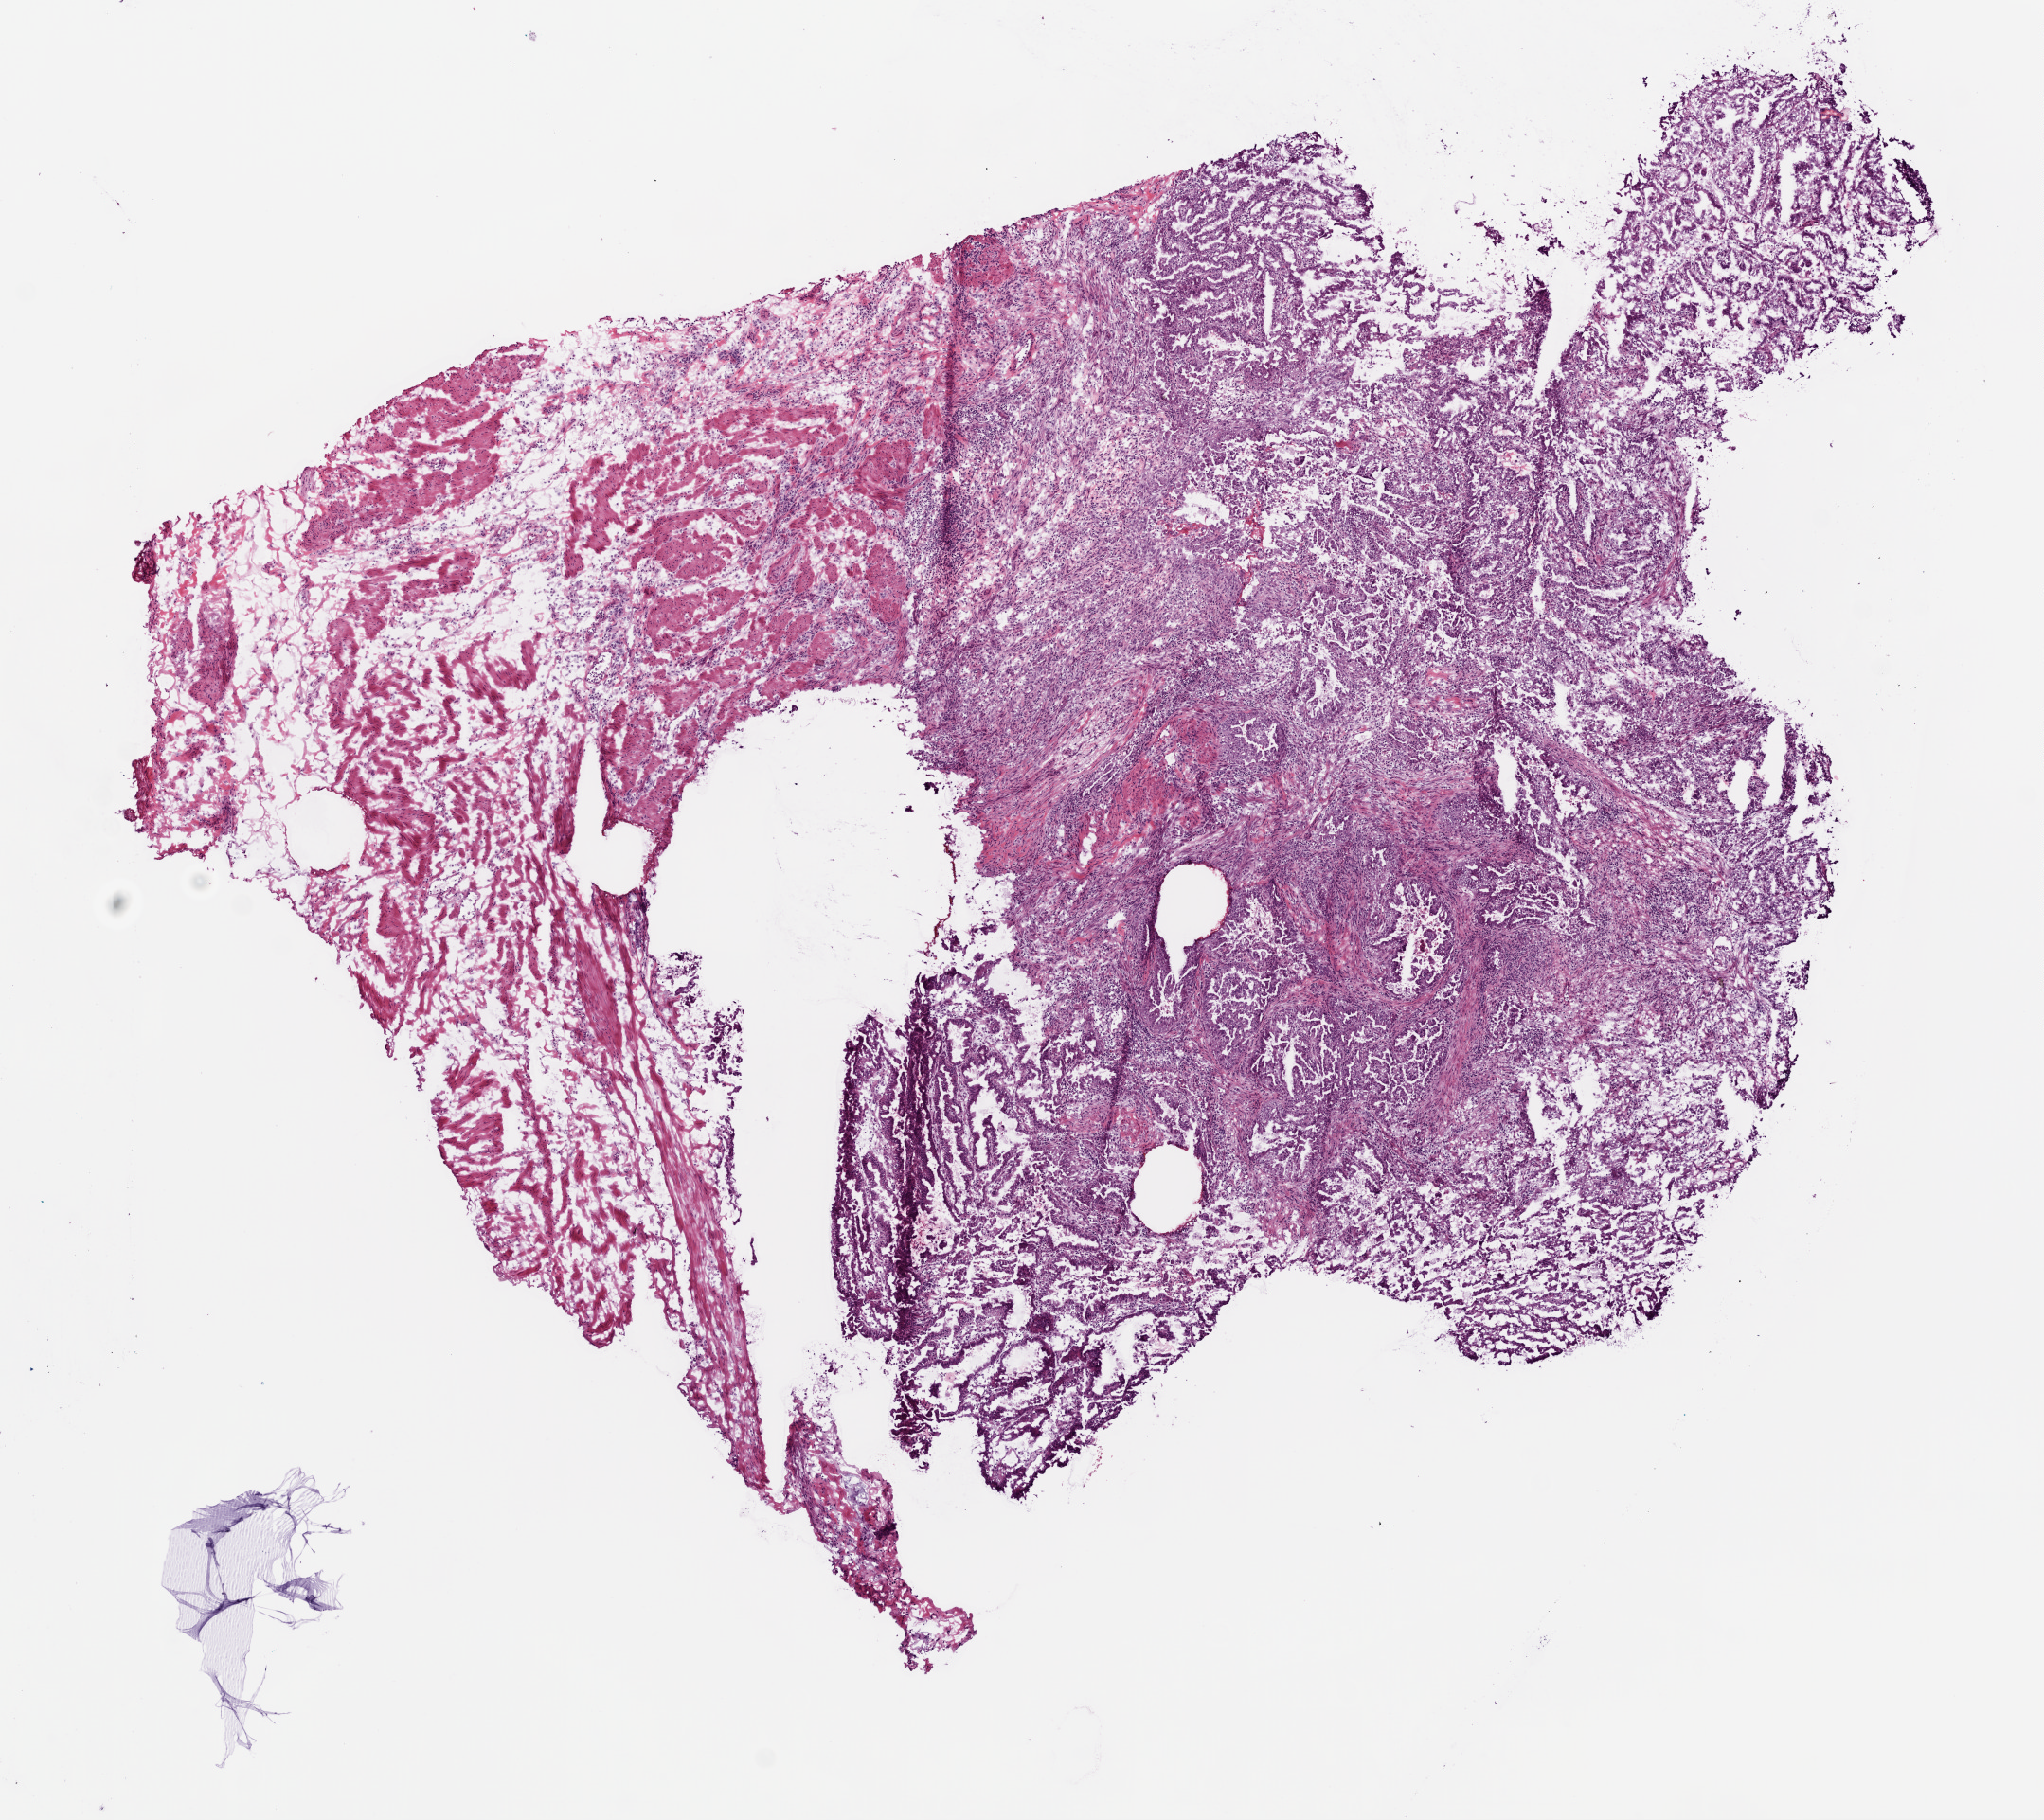
Hematoxylin and eosin (H&E) stained whole-slide image, low-resolution overview of the scanned area, about 8.7 x 7.8 mm, frozen section from the top of the tissue portion, primary tumour sample from the stomach. Patient: male, age at initial diagnosis 77 years. Histologic grade: G2 (moderately differentiated). Slide review estimates, as recorded: tumour cells 85%, tumour nuclei 65%, normal cells 0%, stromal cells 15%, necrosis 0%.
Lymph nodes positive (case pathology): 0 of 18 examined. Histologic diagnosis: Adenocarcinoma, NOS (cardia, NOS). AJCC pathologic stage: IB (7th edition).